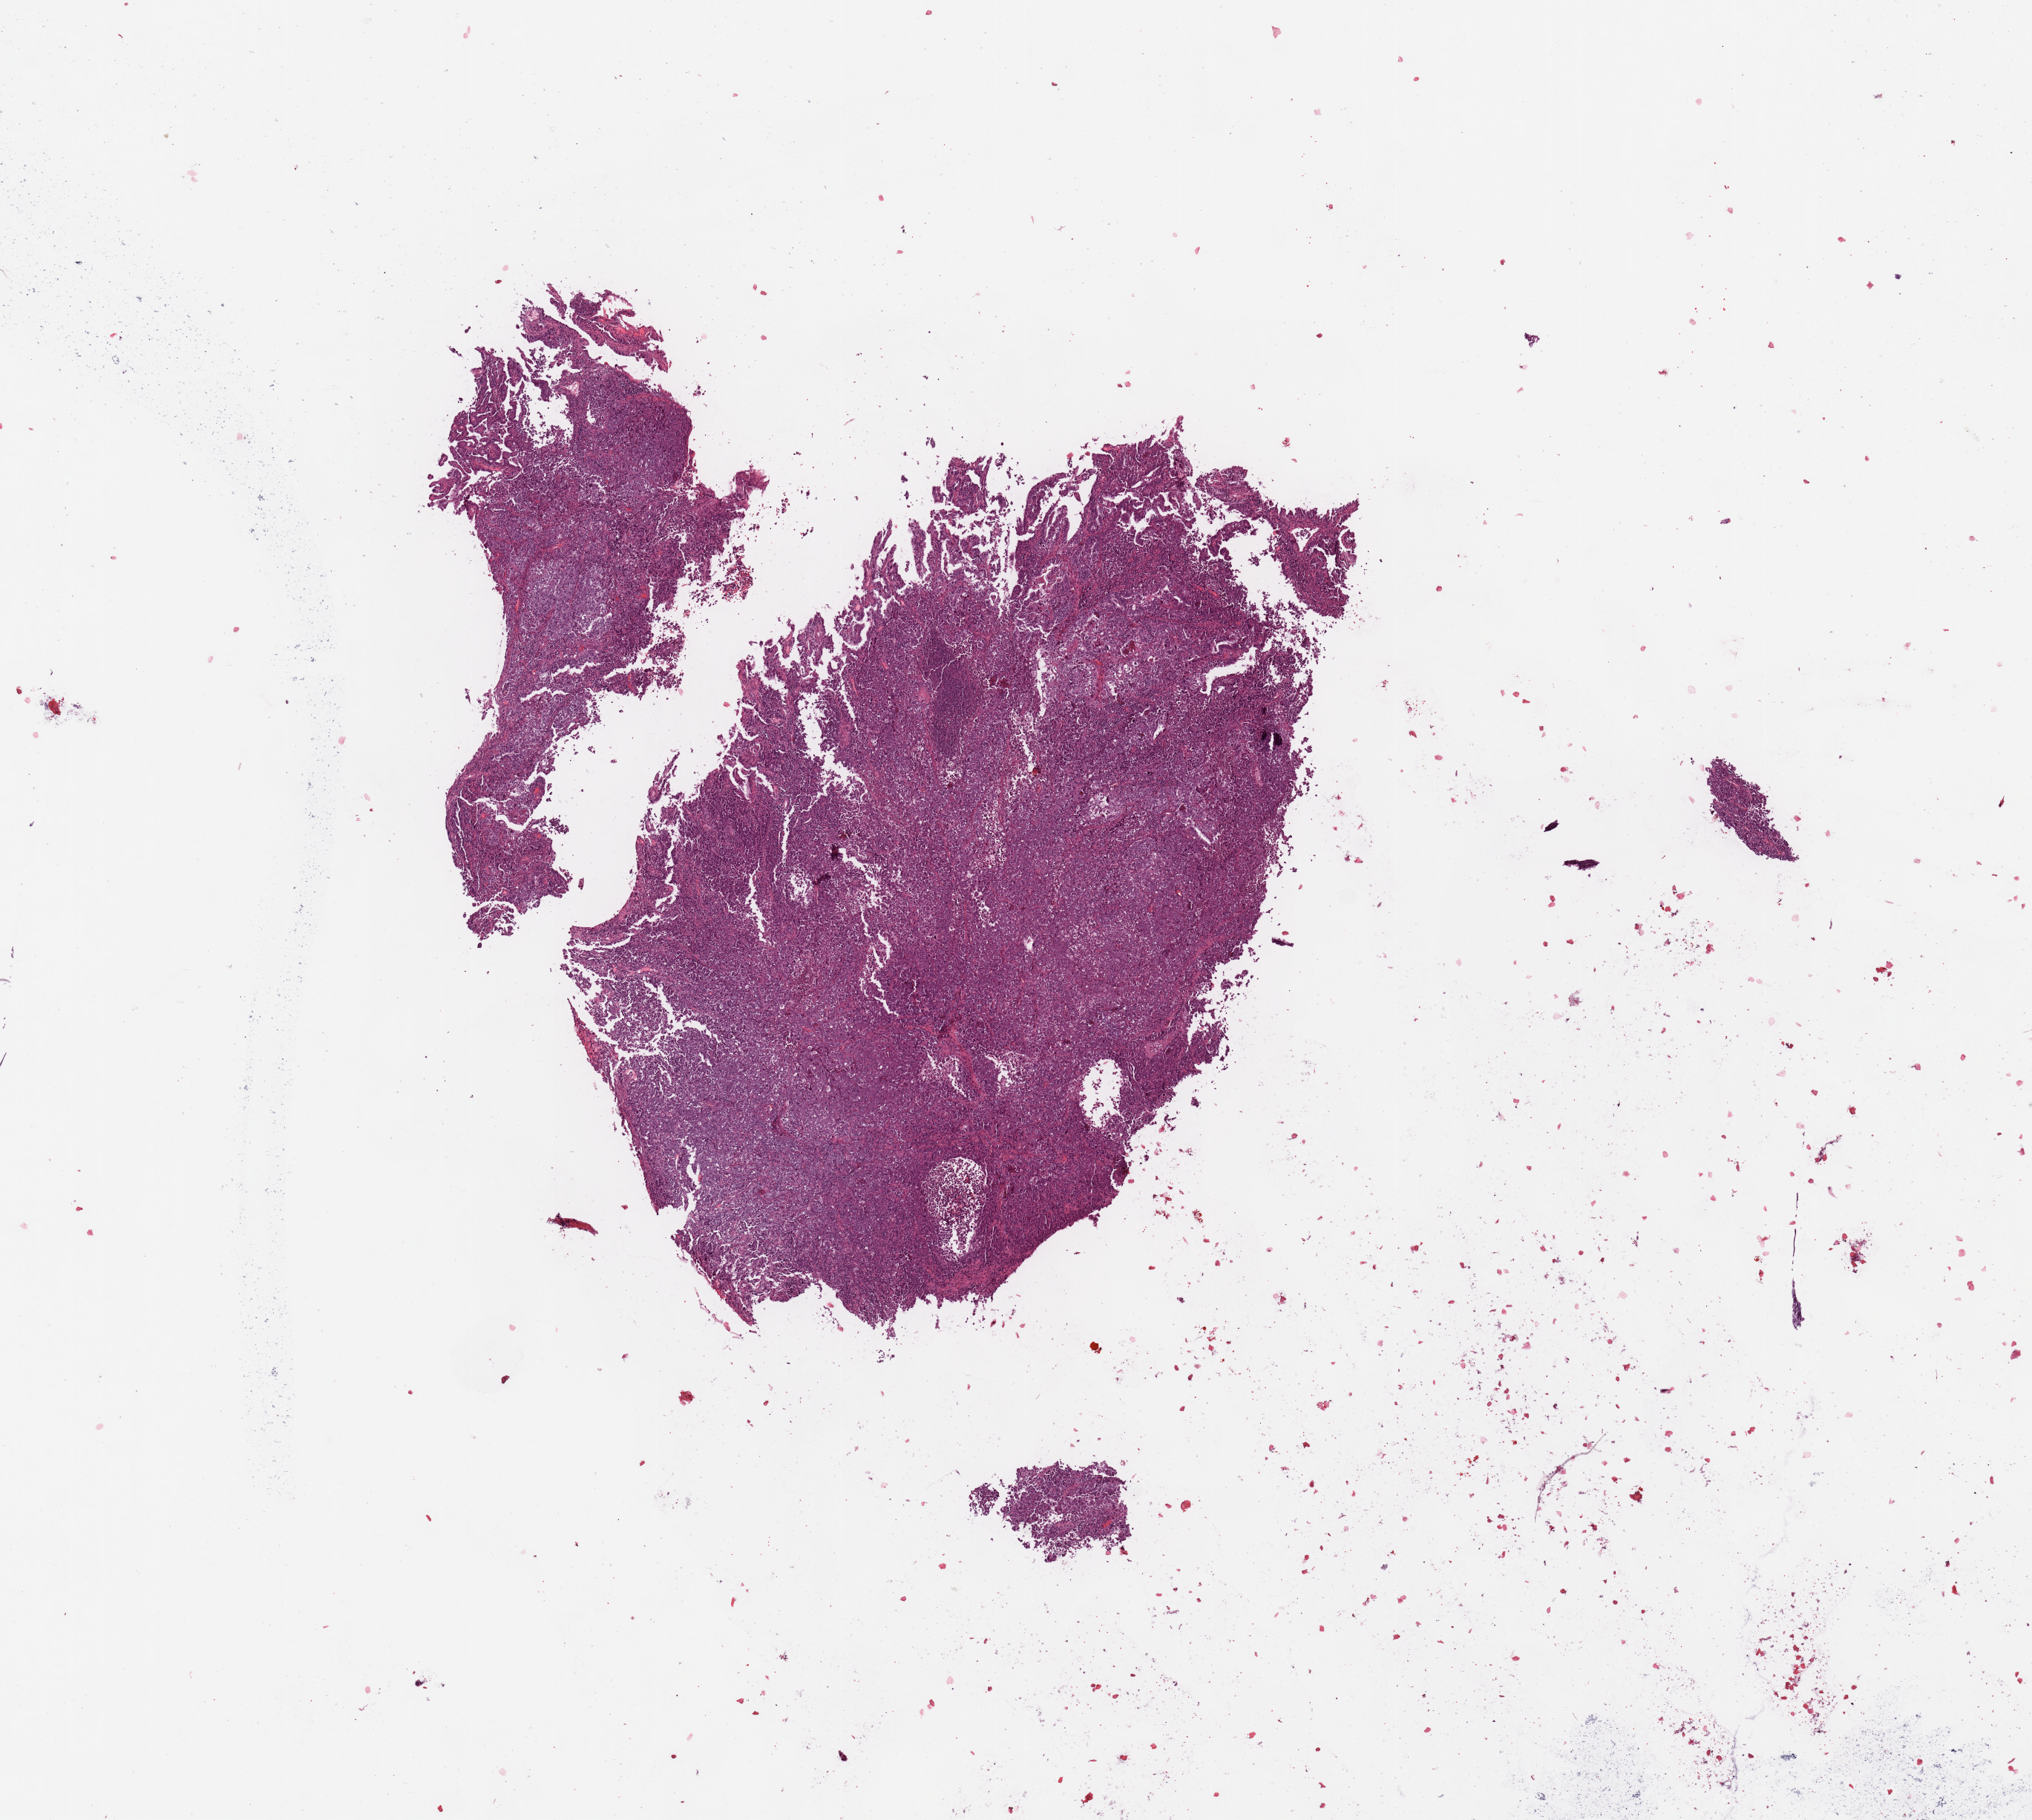
Digitized H&E tissue section (whole slide) — whole scanned area (about 10.8 x 9.7 mm, from a 20x scan) shown as a low-resolution overview. Tumour tissue sample, sampled site: uterus. Female, 73 y/o. Histologic grade: G2 (moderately differentiated). Composition of this section per pathologist review: tumour nuclei 95%, necrosis 0%.
AJCC pathologic stage: IB. Histologic diagnosis: Endometrioid adenocarcinoma, NOS. Primary tumour site (as recorded): posterior endometrium.